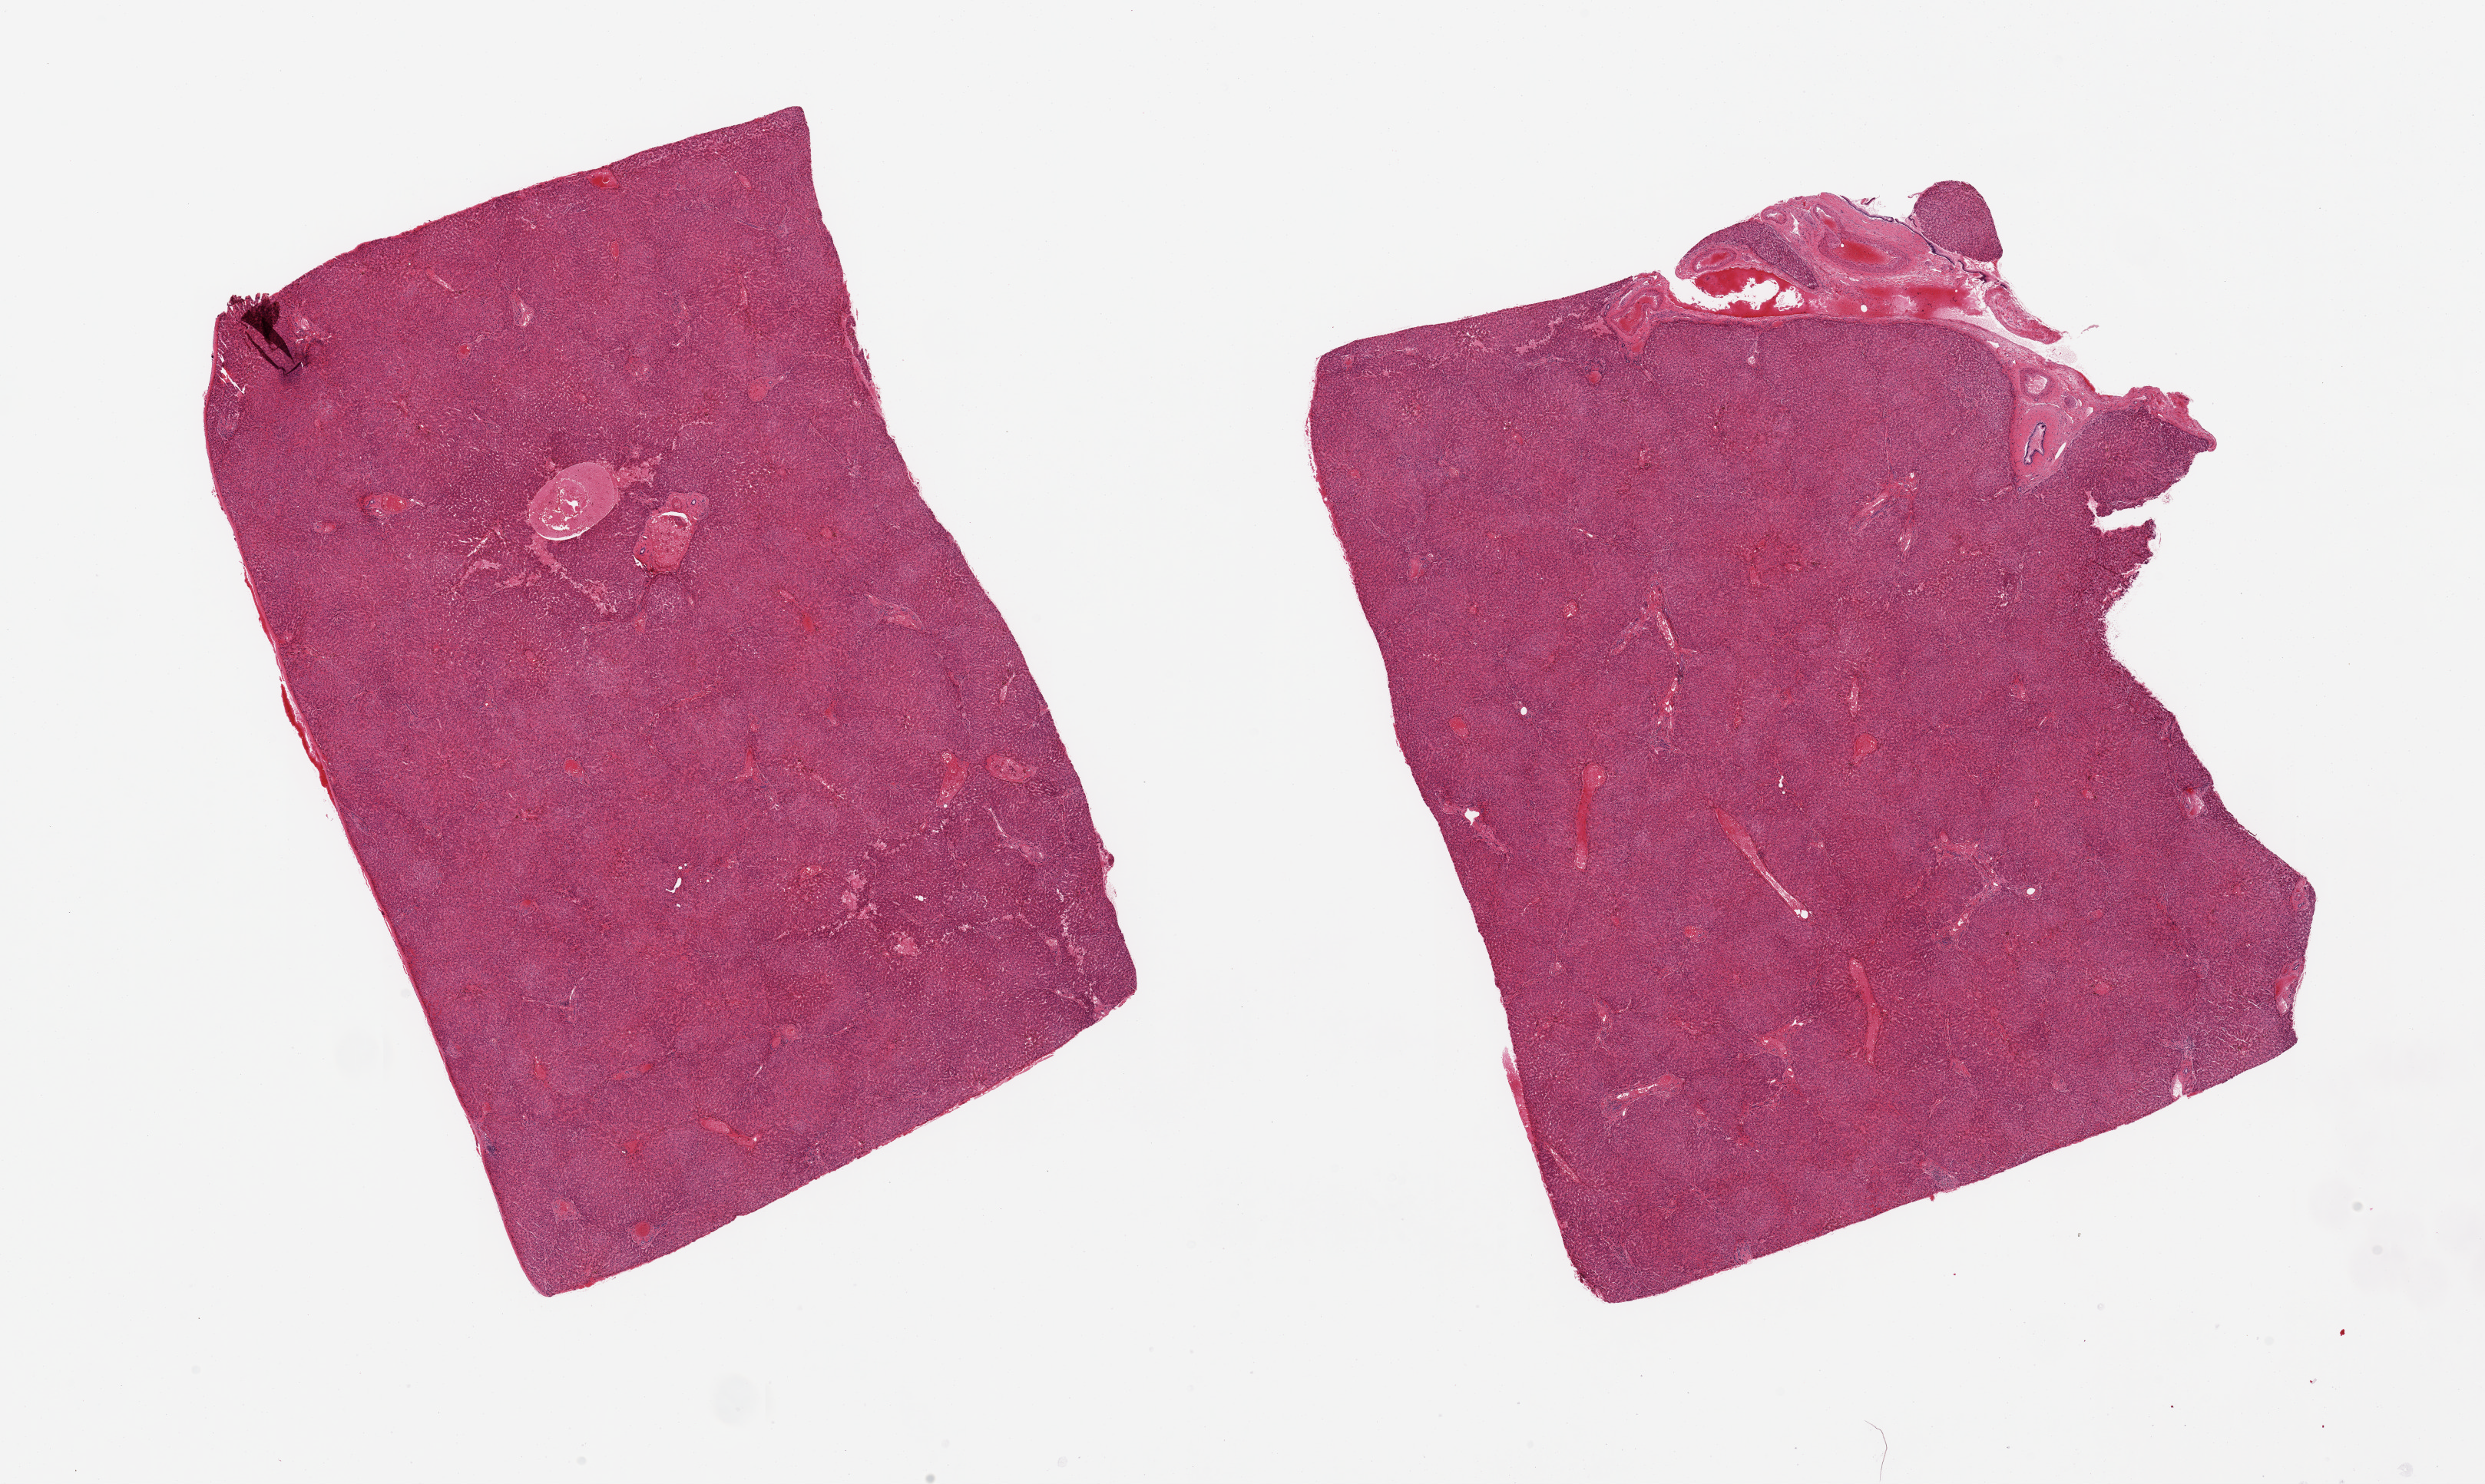
Digitized haematoxylin and eosin-stained section, low-resolution overview of the scanned area, about 25.6 x 15.3 mm (from a 20x scan). PAXgene-fixed paraffin-embedded (PFPE) section. Target tissue: liver. Tissue donor sample. Donor: female.
- pathologist's review note for this sample: 2 pieces; one piece includes capsule (target is 1cm below capsule), one includes larger vessel/duct (to be avoided)